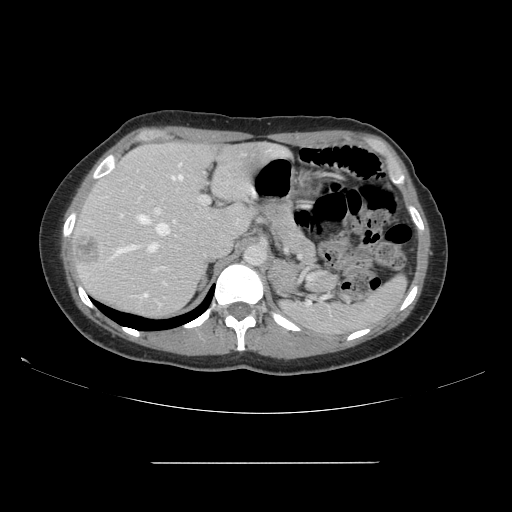
Contrast-enhanced abdominal CT, one axial slice. Position 106 of 151 along the scan axis. 120 kVp. Intravenous contrast given. Soft-tissue window (W 400 / L 40 HU). 2.5 mm slice thickness. 512 × 512 image matrix, field of view 421 × 421 mm. Female patient, age 46 years. From the clinical record (not read from this slice): diagnosis: colorectal cancer liver metastases, imaged before liver resection; multiple liver metastases: yes; largest metastasis: 3 cm; disease in both lobes: yes.
Annotated regions visible in this slice (expert manual segmentation):
- hepatic veins: bounding box <113,164,183,257> (left, top, right, bottom; pixels)
- liver: <72,143,281,318>
- planned liver remnant (the part of the liver to remain after resection): <89,143,282,254>
- portal vein (with intrahepatic branches): <141,185,209,298>
- liver metastasis: <72,236,101,266>
- liver metastasis: <211,148,226,157>